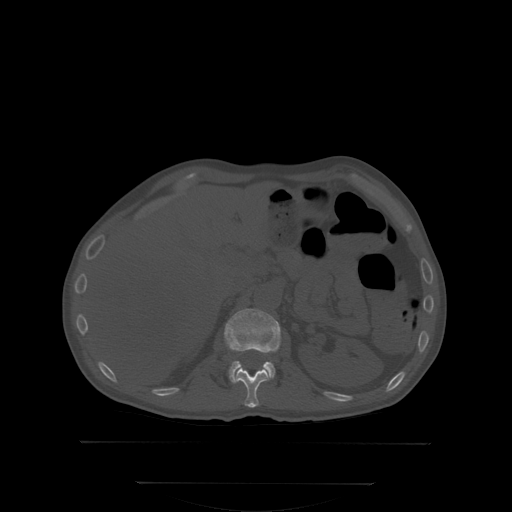
CT including the spine, one axial slice; position 161 of 350 along the scan axis; bone window (W 1800 / L 400 HU); 2.5 mm slice thickness; 512 × 512 image matrix, field of view 500 × 500 mm. Patient: male, 58 years. Case-level facts recorded for this patient, not image findings: primary cancer: prostate; vertebrae with lytic lesions (as recorded): L1.
Outlined on this slice (semi-automatic segmentation, software-assisted and operator-edited):
- L1 vertebra: bounding box (x1, y1, x2, y2) in pixels: (226, 309, 280, 381)
- T12 vertebra: (234, 366, 270, 408)